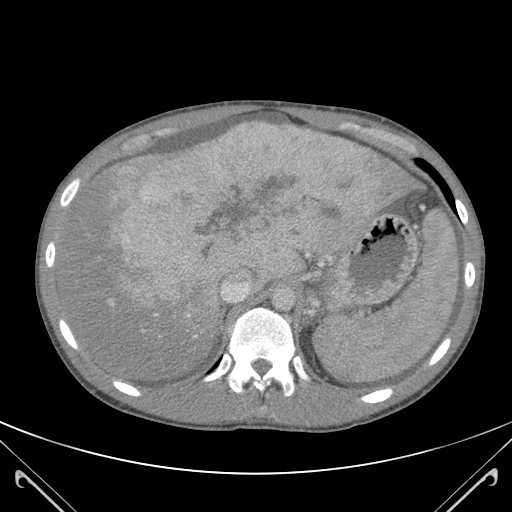
Contrast-enhanced abdominal CT (liver protocol), one axial slice. Slice 88 of 118 in the series (ordered by position). 120 kVp. Soft-tissue window (W 400 / L 40 HU). 3 mm slice thickness. 512 × 512 image matrix, field of view 380 × 380 mm. From the clinical record (not read from this slice): diagnosis: hepatocellular carcinoma (patient treated with transarterial chemoembolisation; whether this scan precedes or follows treatment is not stated here); TNM stage (as recorded): Stage-IIIB; Child-Pugh class: A; tumour nodularity: uninodular.
Structures marked on this image (semi-automatically segmented with operator editing):
- abdominal aorta: bounding box [x1, y1, x2, y2] px = [273, 287, 298, 311]
- liver parenchyma outside the tumour (the mass and vessels are separate outlines, so this box may not span the whole liver): [61, 124, 422, 378]
- mass: [97, 125, 414, 325]
- liver vessels: [112, 281, 251, 338]